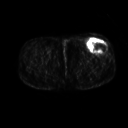
FDG PET of an extremity soft-tissue mass (from a PET/CT study), one axial slice; slice 242 of 267 in the series (ordered by position); 3.27 mm slice thickness; 128 × 128 image matrix, field of view 500 × 500 mm. Patient: male, 64 years. Case-level facts recorded for this patient, not image findings: histological type: extraskeletal osteosarcoma; grade: high; site of the primary tumour: thigh.
Outlined on this slice (expert contour drawn on MRI and transferred to this co-registered scan by the dataset authors):
- gross tumour volume (mass): bounding box <87,40,107,53> (left, top, right, bottom; pixels)